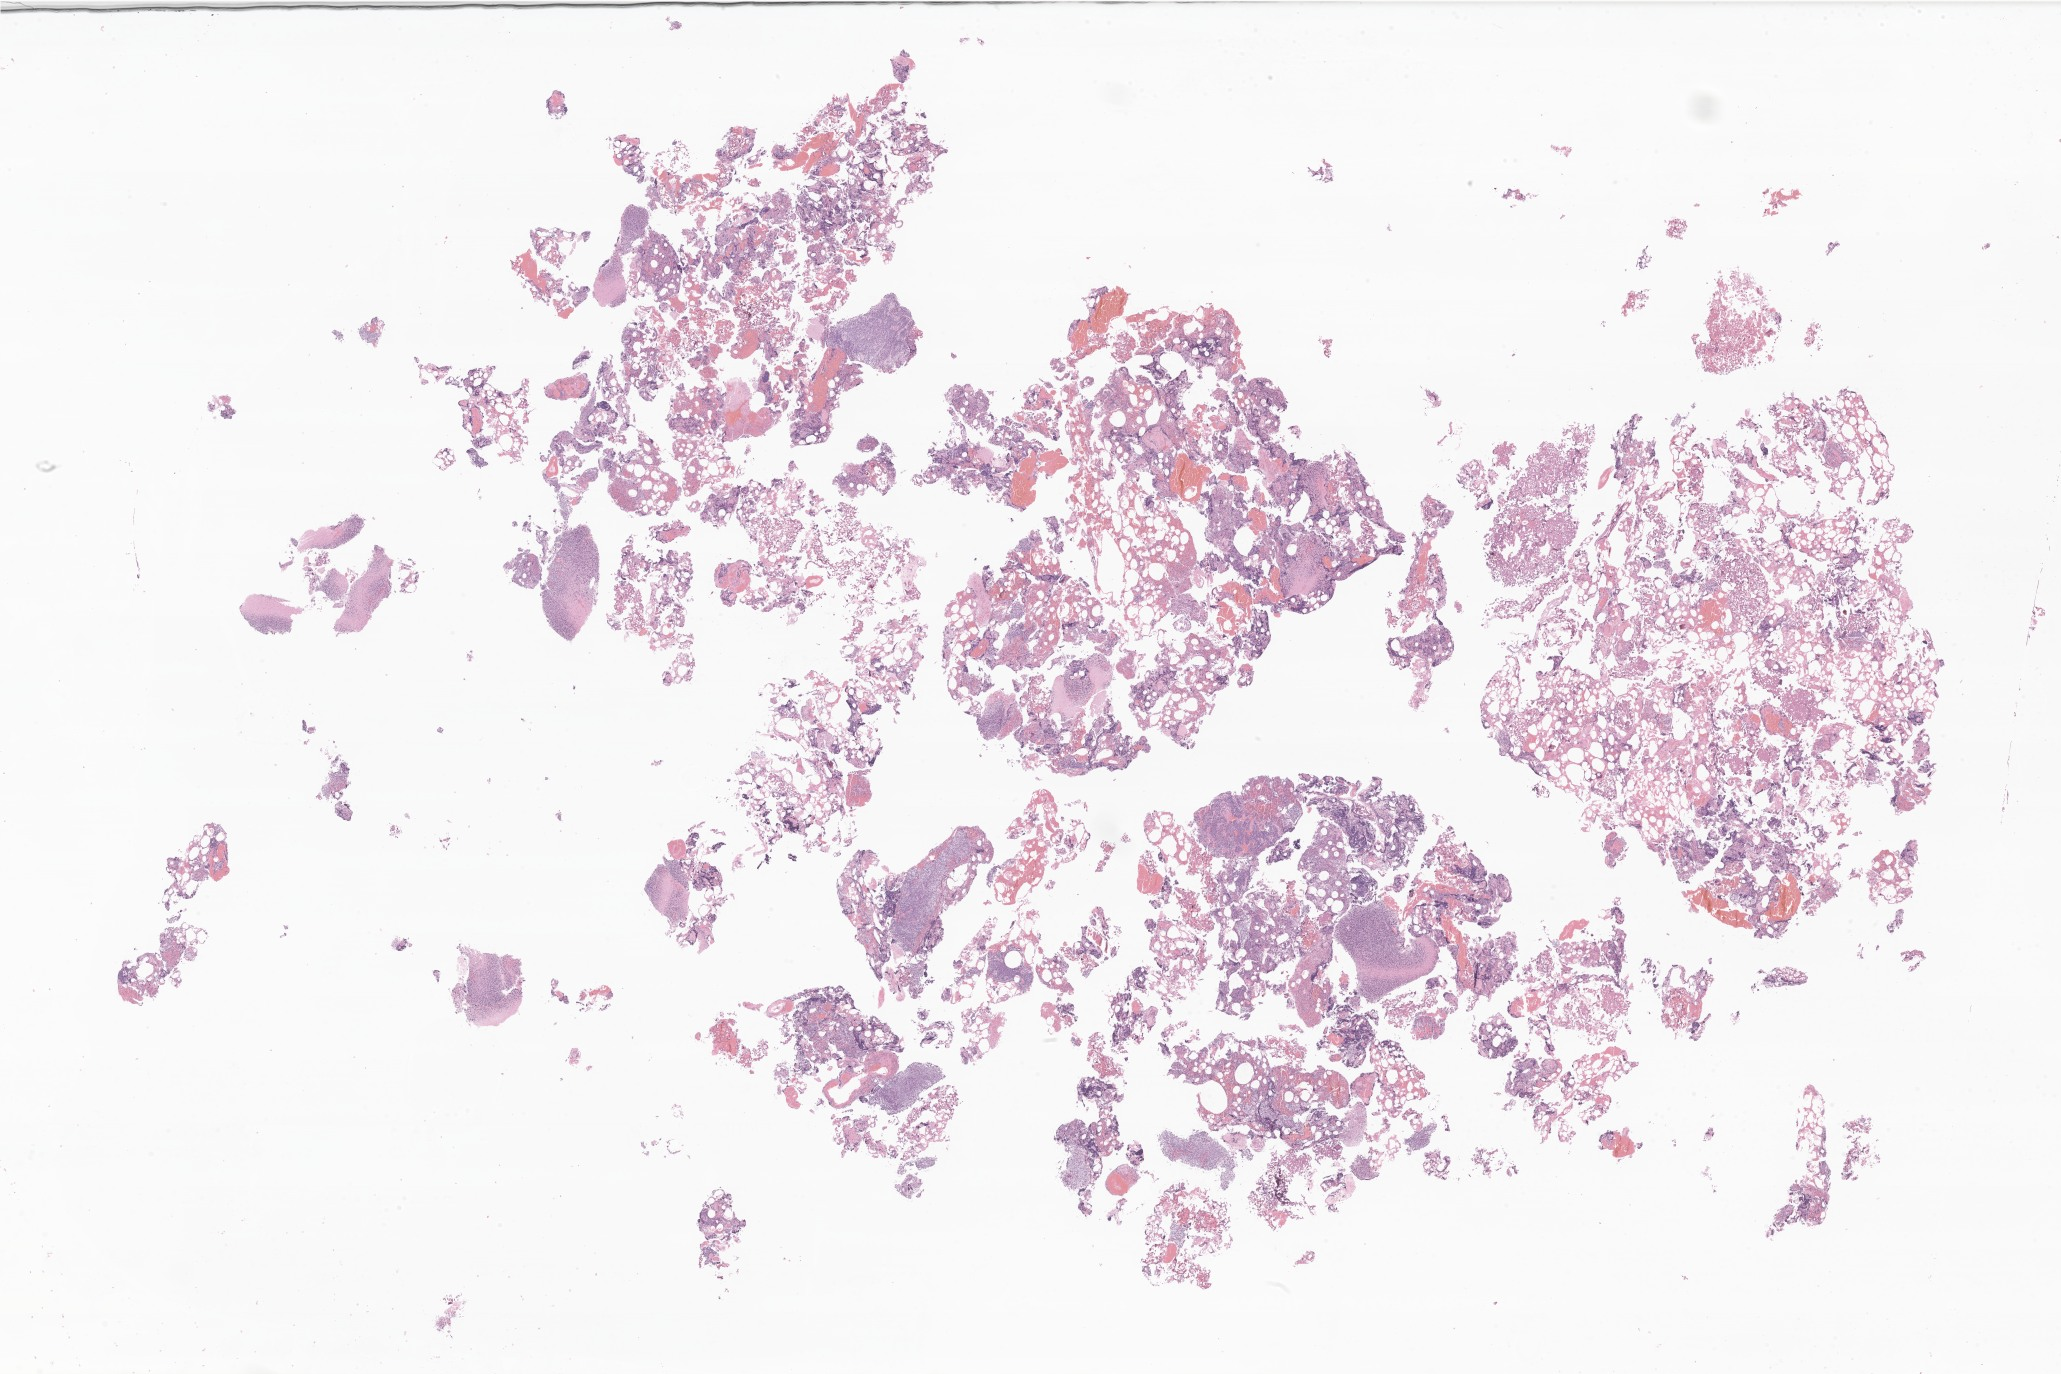
Hematoxylin and eosin (H&E) whole-slide image of tumor tissue from the brain, a low-resolution overview of the entire scanned area, about 34.8 x 23.2 mm. FFPE section. Male patient, age 95 months (7 years 11 months).
Recorded diagnosis: Medulloblastoma, NOS.